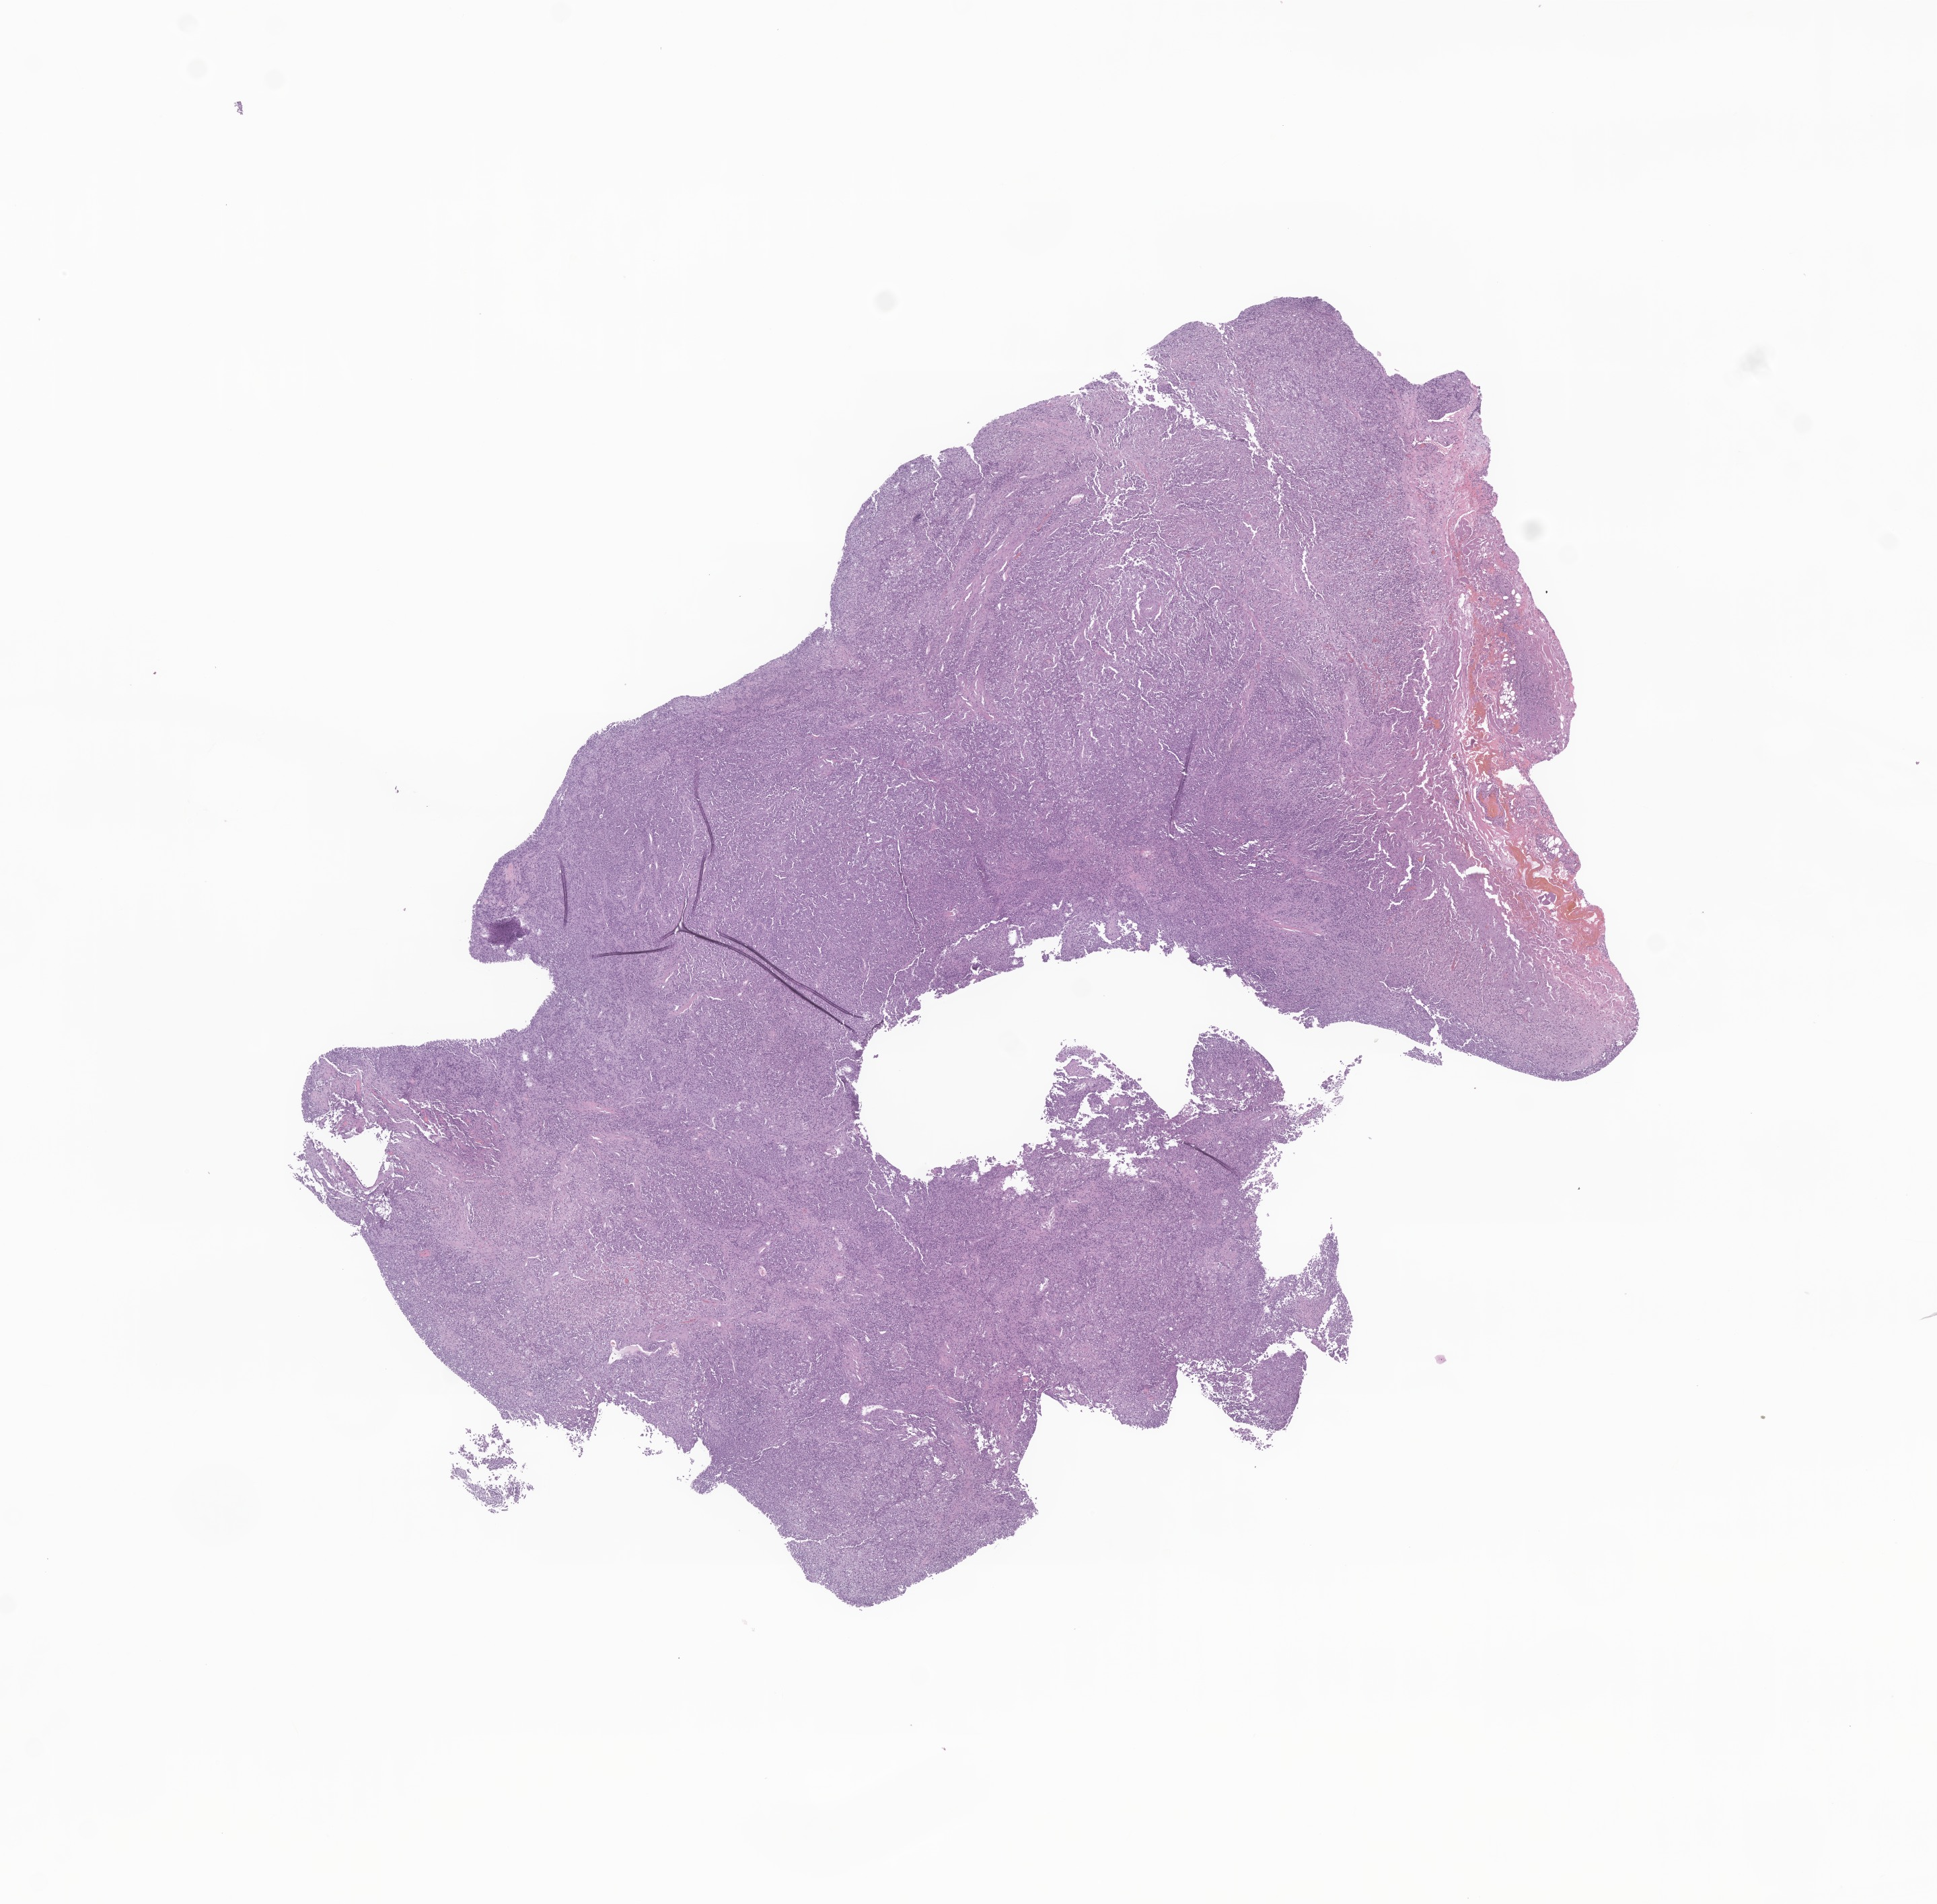
Haematoxylin and eosin whole-slide image of tumor tissue from the lower limb, shown as a low-resolution overview of the whole scanned area (about 12.1 x 11.9 mm). Formalin-fixed paraffin-embedded section. Patient: male, age 761 days (about 2.1 years).
Diagnosis (ICD-O-3 morphology term): Rhabdoid tumor, NOS.